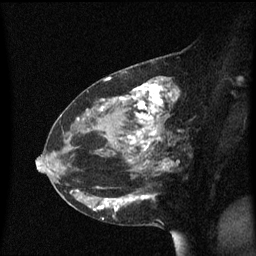
Breast MRI (dynamic contrast-enhanced), one sagittal slice. Dynamic contrast-enhanced series, image 2 of 3 at this slice position (ordered by acquisition). 1.5 T. TE 4.2 ms, TR 8.4 ms. 2 mm slice thickness. 256 × 256 image matrix, field of view 200 × 200 mm. Female patient, age 48 years. Case-level facts recorded for this patient, not image findings: setting: breast cancer imaged before/during neoadjuvant chemotherapy; receptor status: HR-positive, HER2-negative.
Annotated regions visible in this slice (semi-automatically segmented with operator editing):
- analysis volume of interest (the breast-tissue region the enhancement analysis was run in; not a lesion): box from (x=80, y=78) to (x=185, y=221) px
- tumour enhancement mask (voxels above the 70 % enhancement threshold inside the analysis volume of interest): (x=88, y=81)–(x=181, y=221)